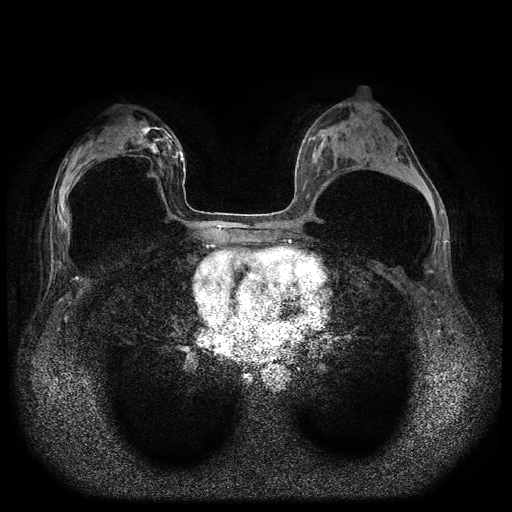
Breast MRI (dynamic contrast-enhanced, multi-phase), one axial slice. Position 45 of 116 along the scan axis. Dynamic contrast-enhanced series, time point 2 of 5 at this slice position (early post-contrast). 1.5 T. TE 2.6 ms, TR 5.4 ms. 2 mm slice thickness. 512 × 512 image matrix. Patient: female, 42 years.
Annotated regions visible in this slice (semi-automatically segmented with operator editing):
- breast lesion (labelled 'tumour' in the annotation; benign lesions carry a separate 'benign' label): box from (x=138, y=126) to (x=160, y=154) px